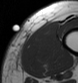
MRI of an extremity soft-tissue mass, one axial slice. Position 6 of 43 along the scan axis. MR volume resampled by the dataset authors to the PET/CT grid (not the native acquisition matrix). 78 × 83 image matrix. Male patient. Case-level facts recorded for this patient, not image findings: histological type: pleiomorphic leiomyosarcoma; grade: high; site of the primary tumour: left thigh.
Structures marked on this image (expert contour drawn on MRI and transferred to this co-registered scan by the dataset authors):
- gross tumour volume including surrounding oedema: box from (x=25, y=21) to (x=58, y=73) px